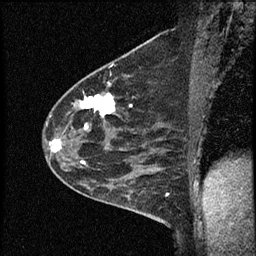
Breast MRI (dynamic contrast-enhanced), one sagittal slice; position 41 of 60 along the scan axis; dynamic contrast-enhanced study with each time point stored as its own series, time point 2 of 4 at this slice position (early post-contrast, ordered by acquisition time); 1.5 T; TE 4.2 ms, TR 17.6 ms; 256 × 256 image matrix, field of view 200 × 200 mm. Female patient, age 53 years. Case-level facts recorded for this patient, not image findings: setting: breast cancer imaged before/during neoadjuvant chemotherapy; receptor status: HR-positive, HER2-negative.
Outlined on this slice (semi-automatically segmented with operator editing):
- analysis volume of interest (the breast-tissue region the enhancement analysis was run in; not a lesion): box from (x=42, y=69) to (x=156, y=199) px
- tumour enhancement mask (voxels above the 100 % enhancement threshold inside the analysis volume of interest): (x=52, y=83)–(x=115, y=163)